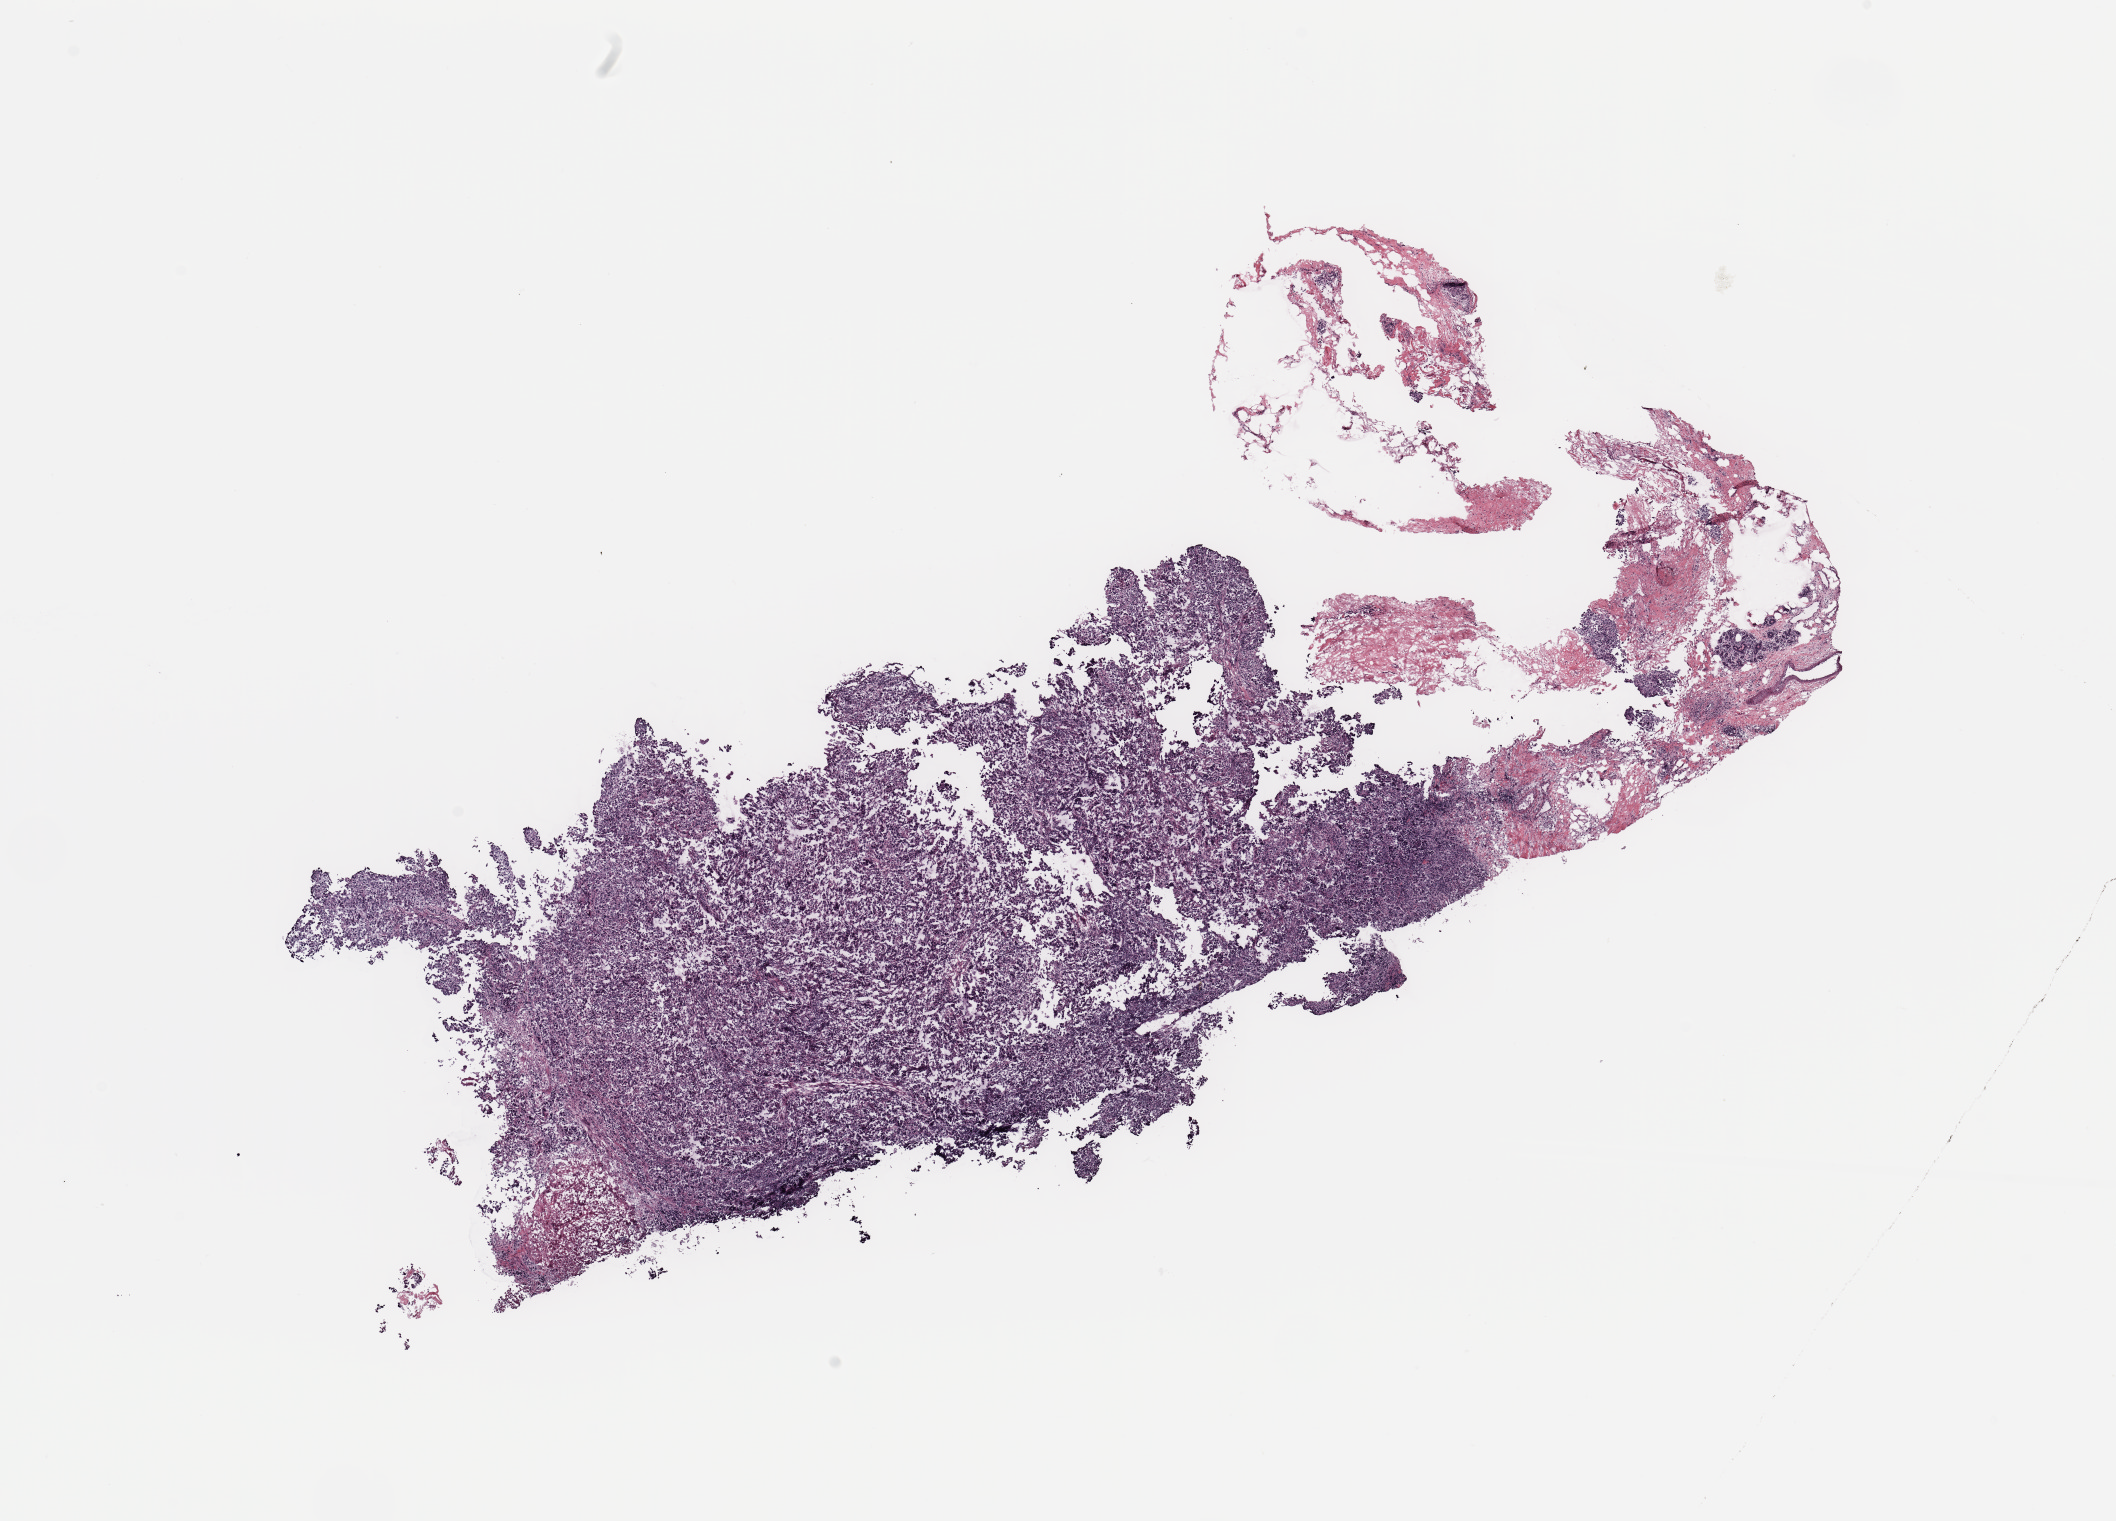
Hematoxylin and eosin (H&E) stained whole-slide image, a low-resolution overview of the entire scanned area, about 16.7 x 12.0 mm. Tumour tissue sample, breast. Patient: female, age 58 years.
Diagnosis: Infiltrating duct carcinoma, NOS. AJCC pathologic stage: II.